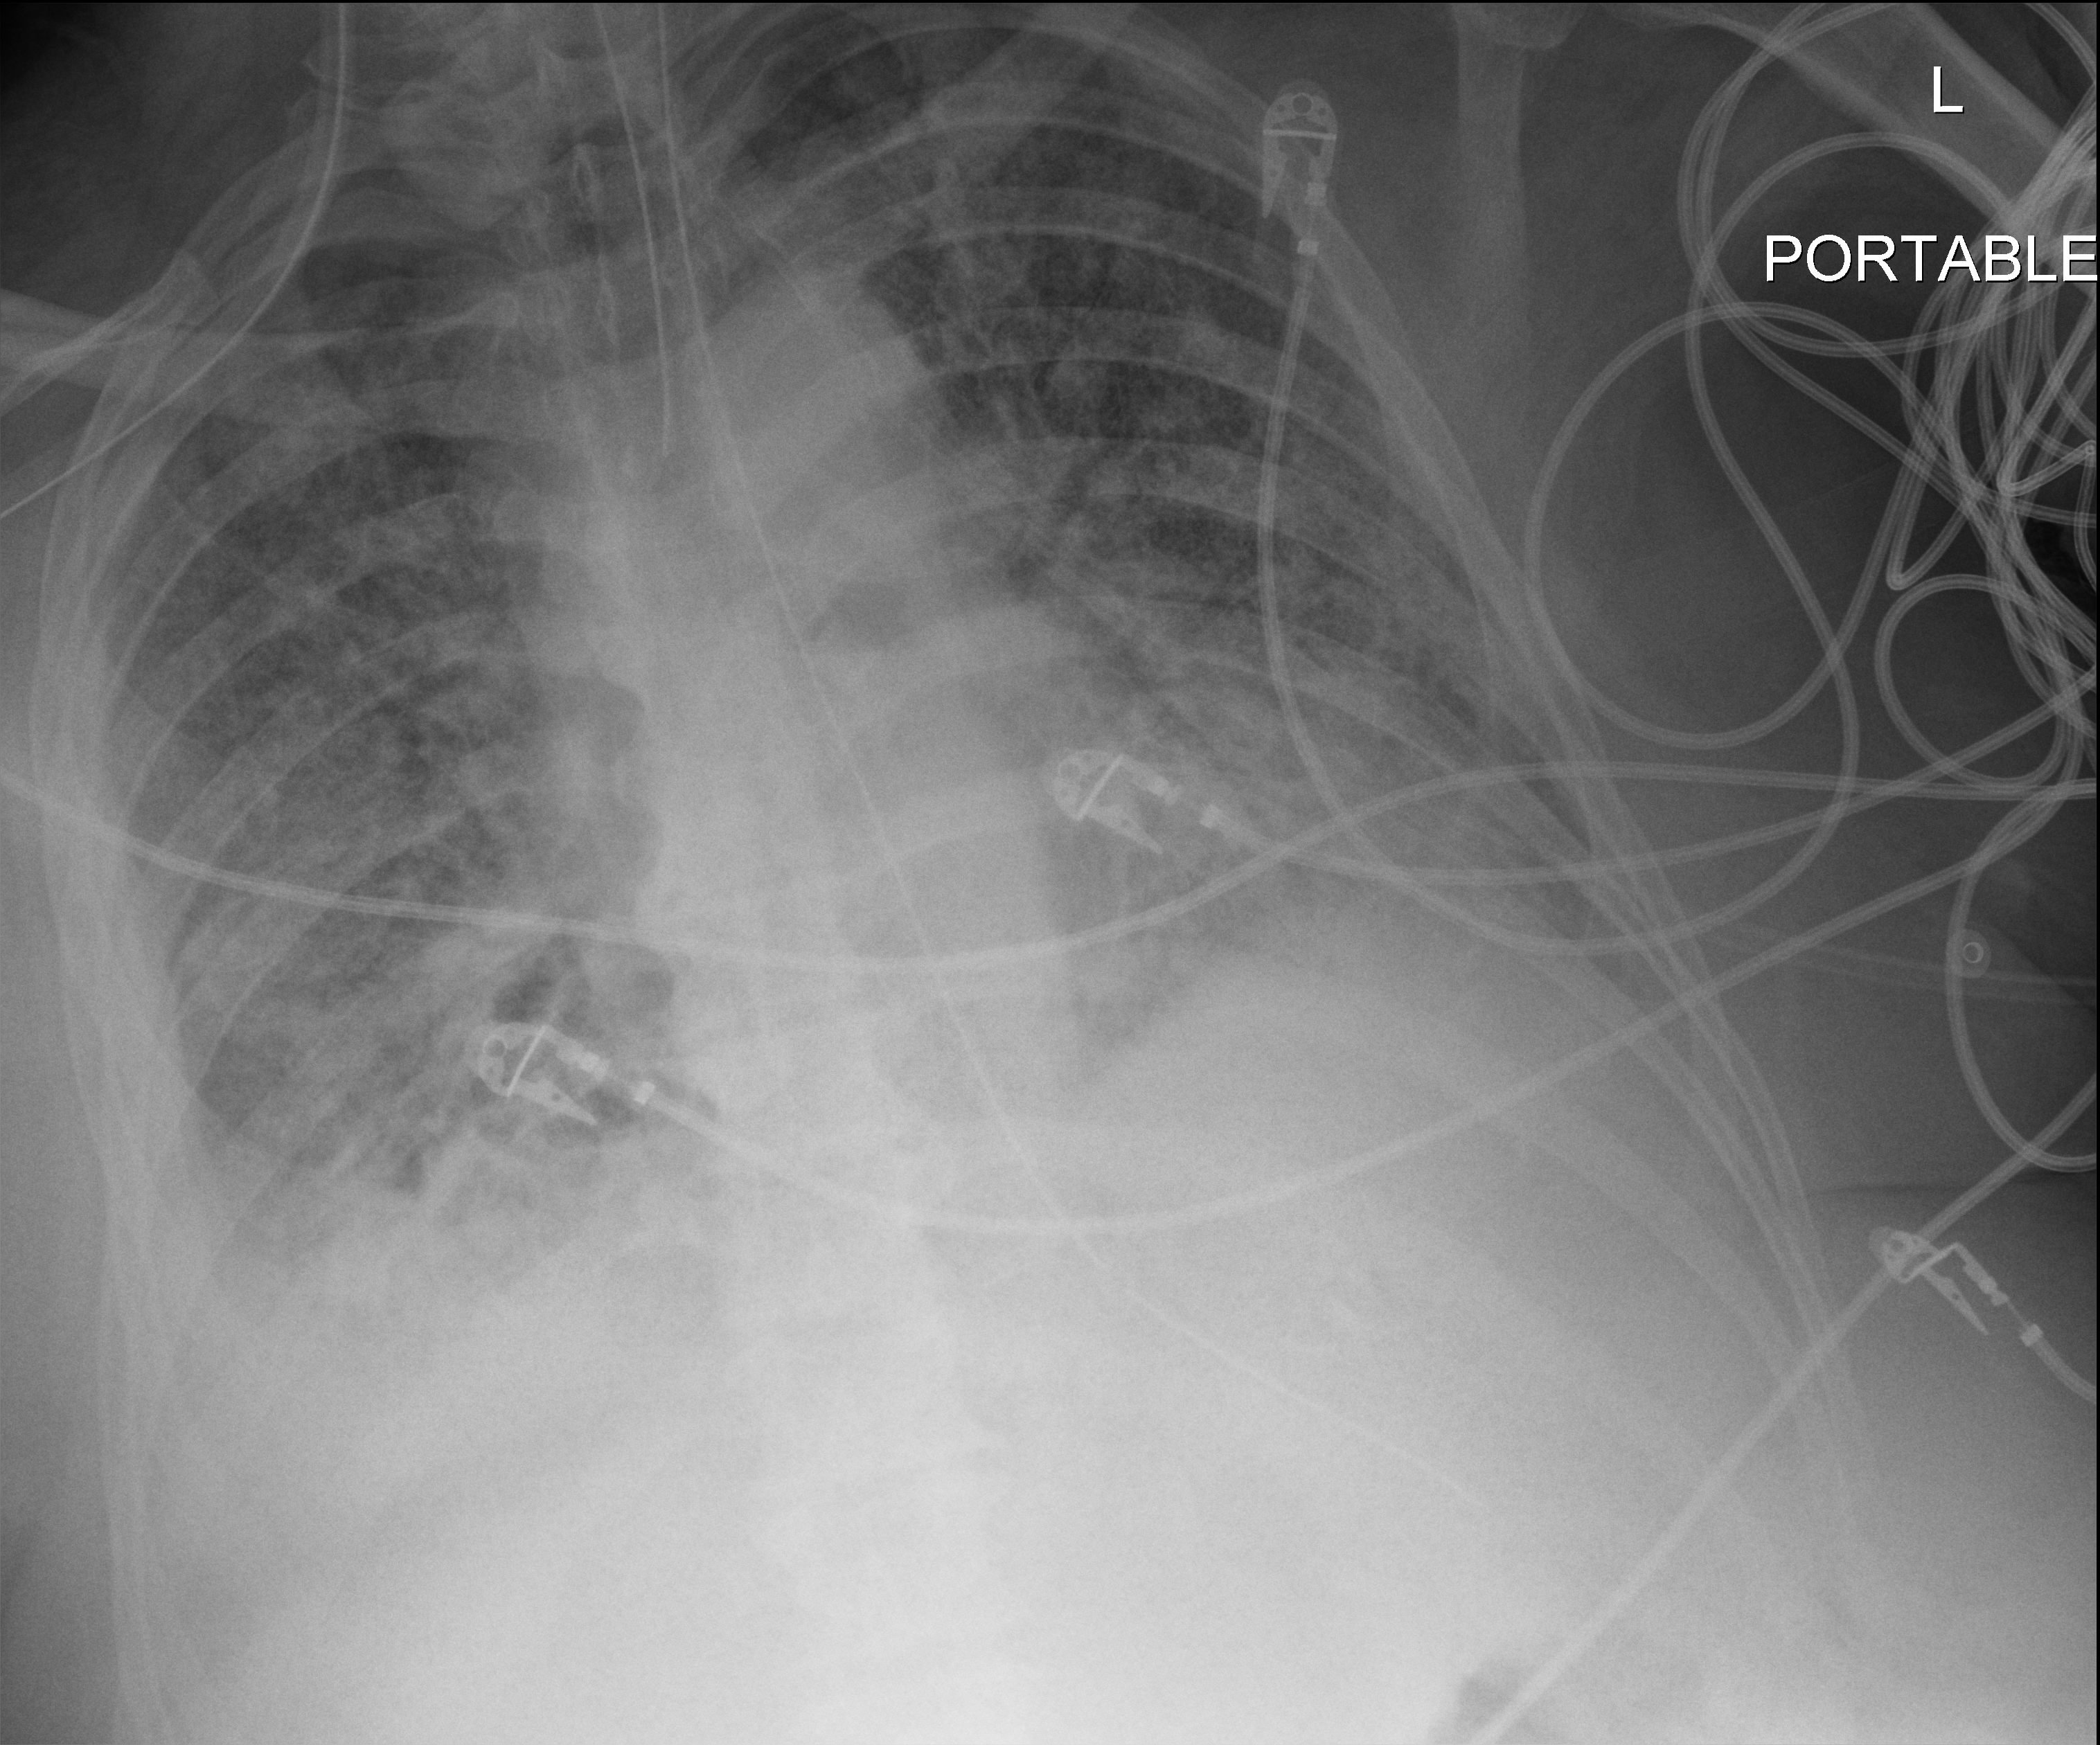
Chest X-ray (portable), anteroposterior (AP) projection. Male patient hospitalised with COVID-19, age 60–74 years.
Admission-level facts for this patient (not findings on this image; timing relative to this image not recorded): diabetes (admission record): no.